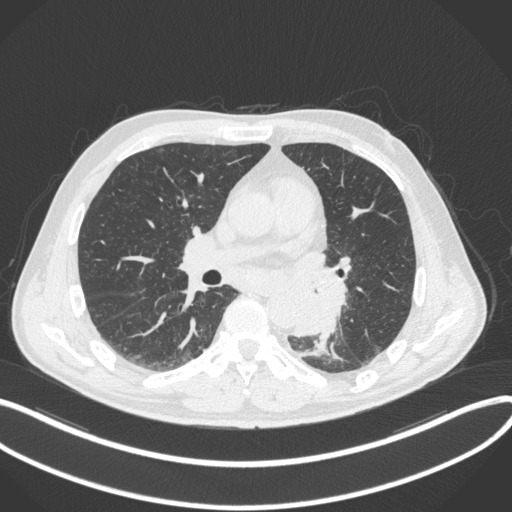
Chest CT, one axial slice. Slice 178 of 328 in the series (ordered by position). Reconstruction kernel B31f. 120 kVp. Lung window (W 1500 / L -600 HU). 1 mm slice thickness. 512 × 512 image matrix, field of view 400 × 400 mm. Male patient, age 59 years. From the clinical record (not read from this slice): clinical TNM (as recorded): T2a N2 M0.
Annotated regions visible in this slice (bounding box drawn by a radiologist):
- lung tumour (recorded histology: squamous cell carcinoma): bounding box [x1, y1, x2, y2] px = [290, 271, 352, 339]